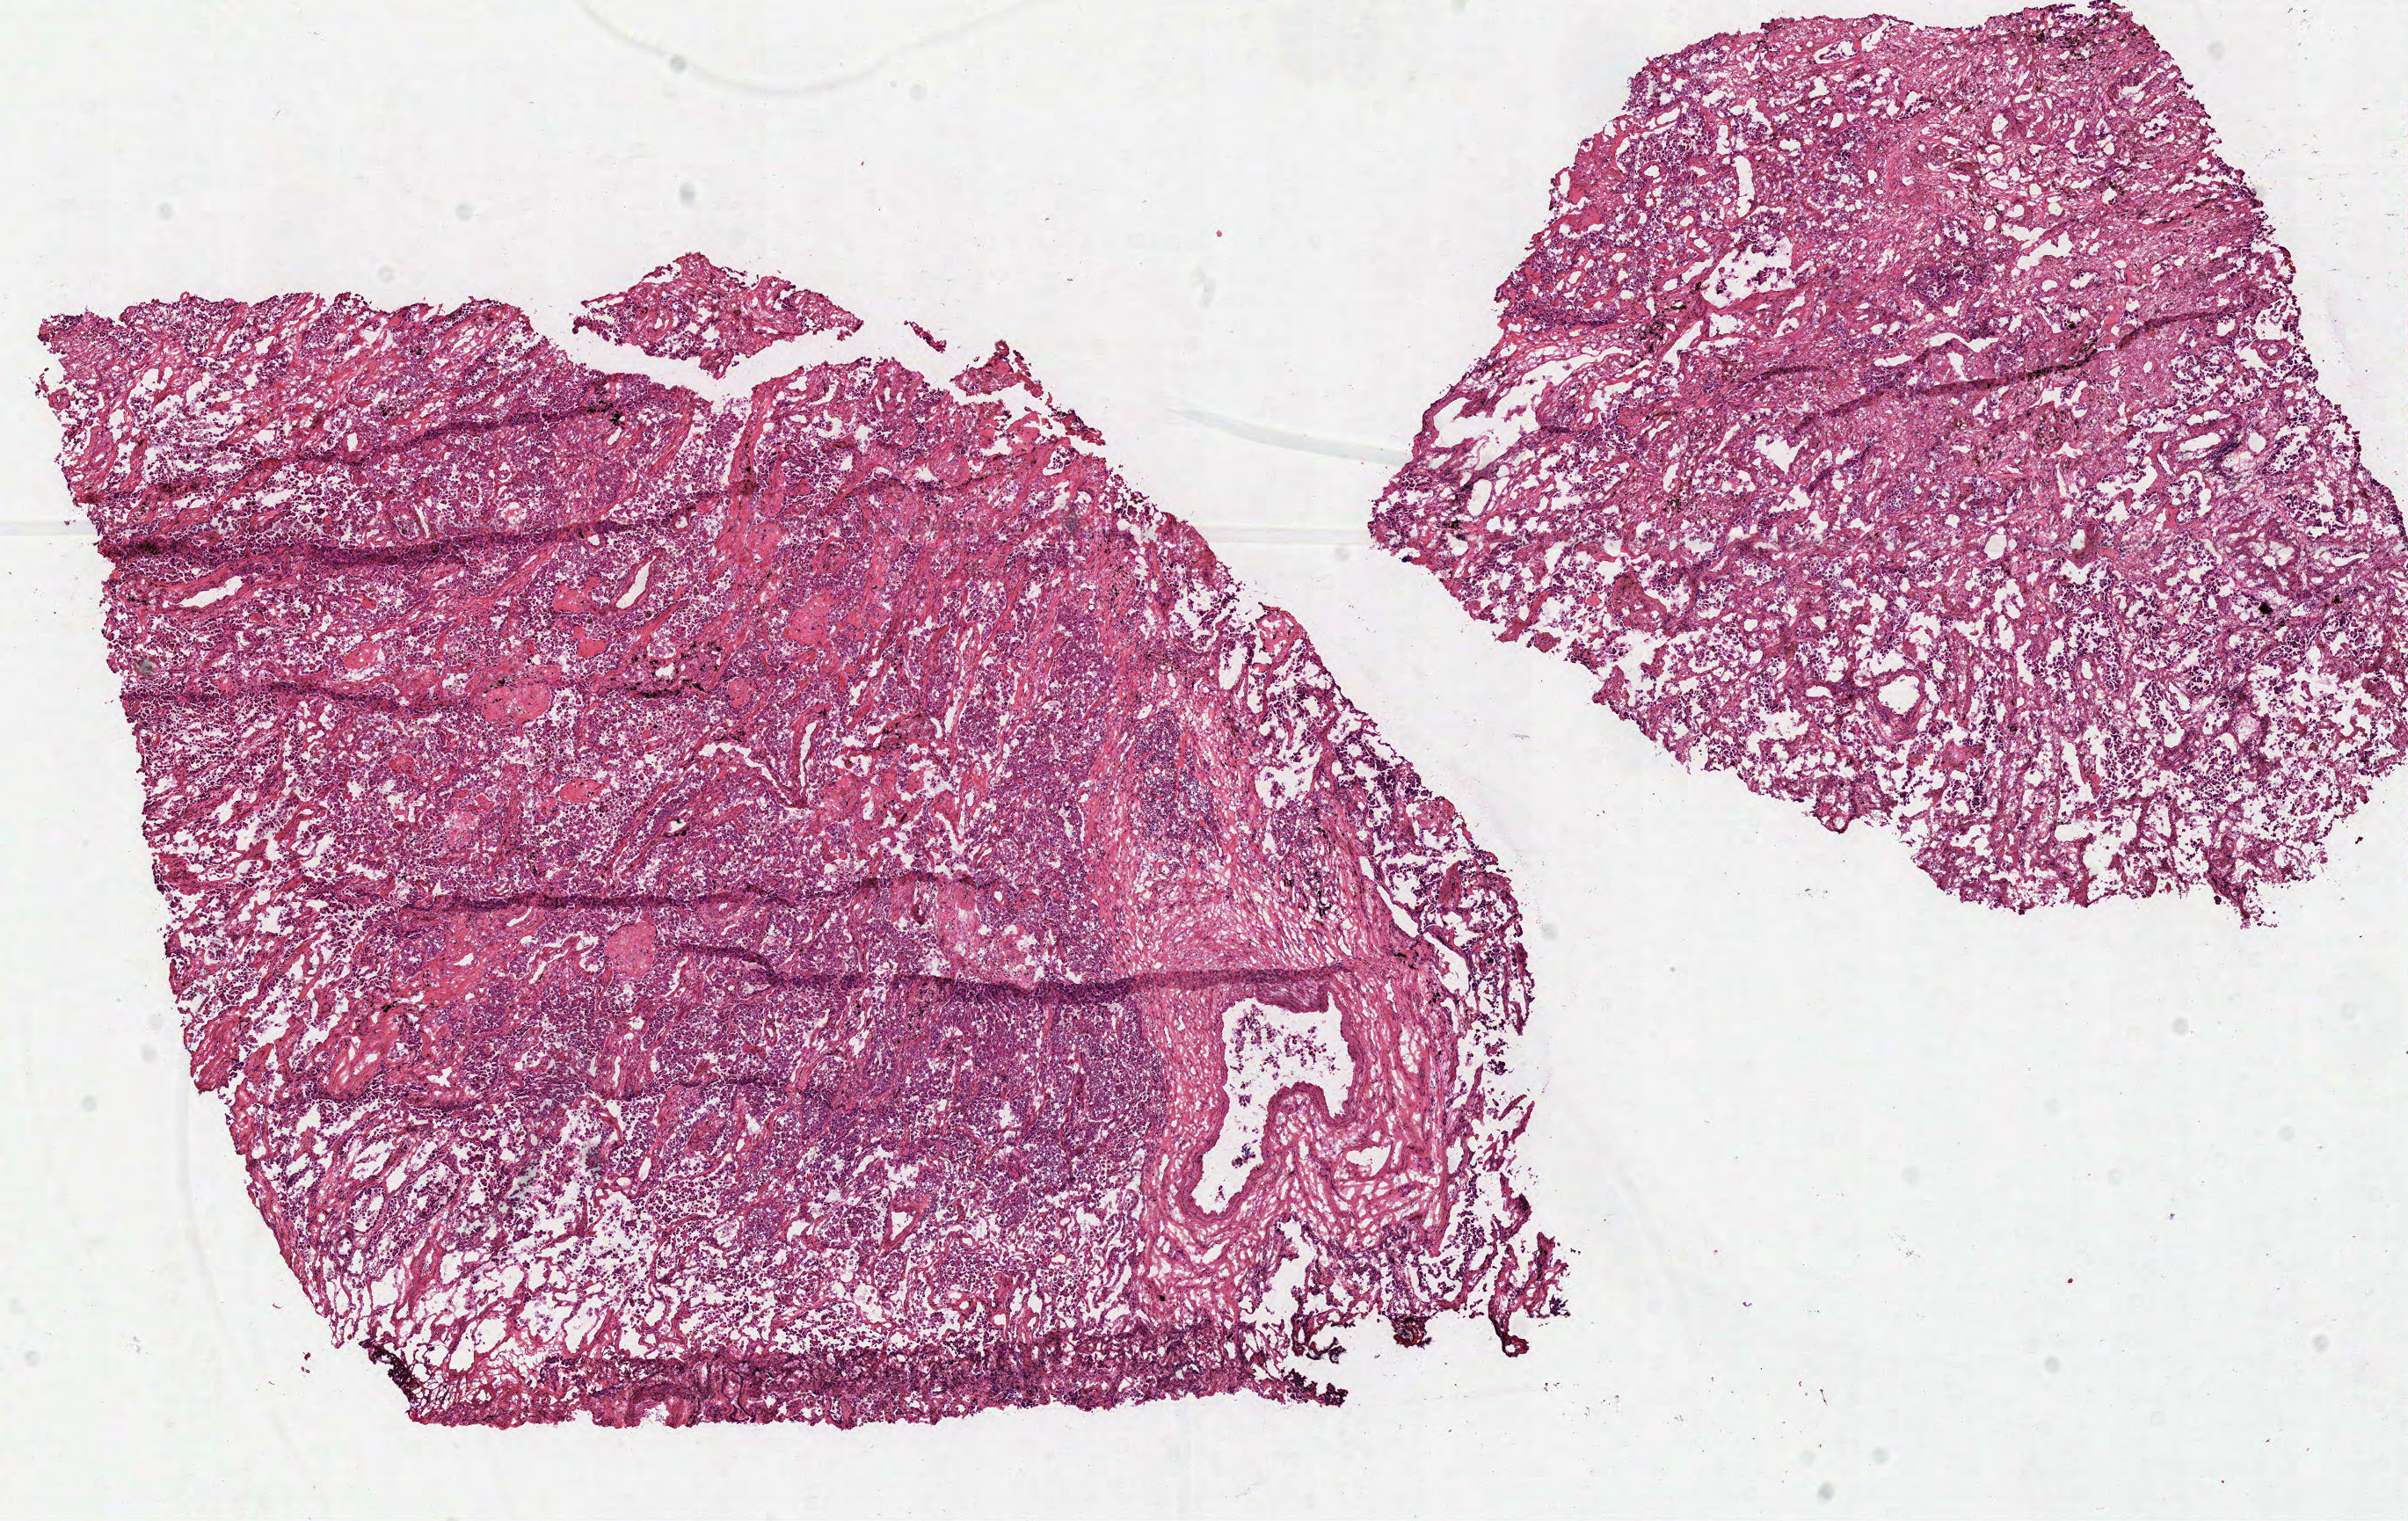
Whole-slide histology image, Hematoxylin and eosin (H&E) stained, a low-resolution overview of the entire scanned area, about 10.8 x 6.8 mm (acquisition: 40x scan). Frozen section from the top of the tissue portion. Primary tumour sample from the lung. Patient: female, age at initial diagnosis 54 years. Pathologist review of this section (percent, as recorded): tumour cells 75%, tumour nuclei 75%, normal cells 10%, stromal cells 10%, necrosis 5%.
AJCC pathologic stage: IIB (7th edition). Diagnosis: Adenocarcinoma, NOS (upper lobe, lung). TNM: T3 N0 MX.